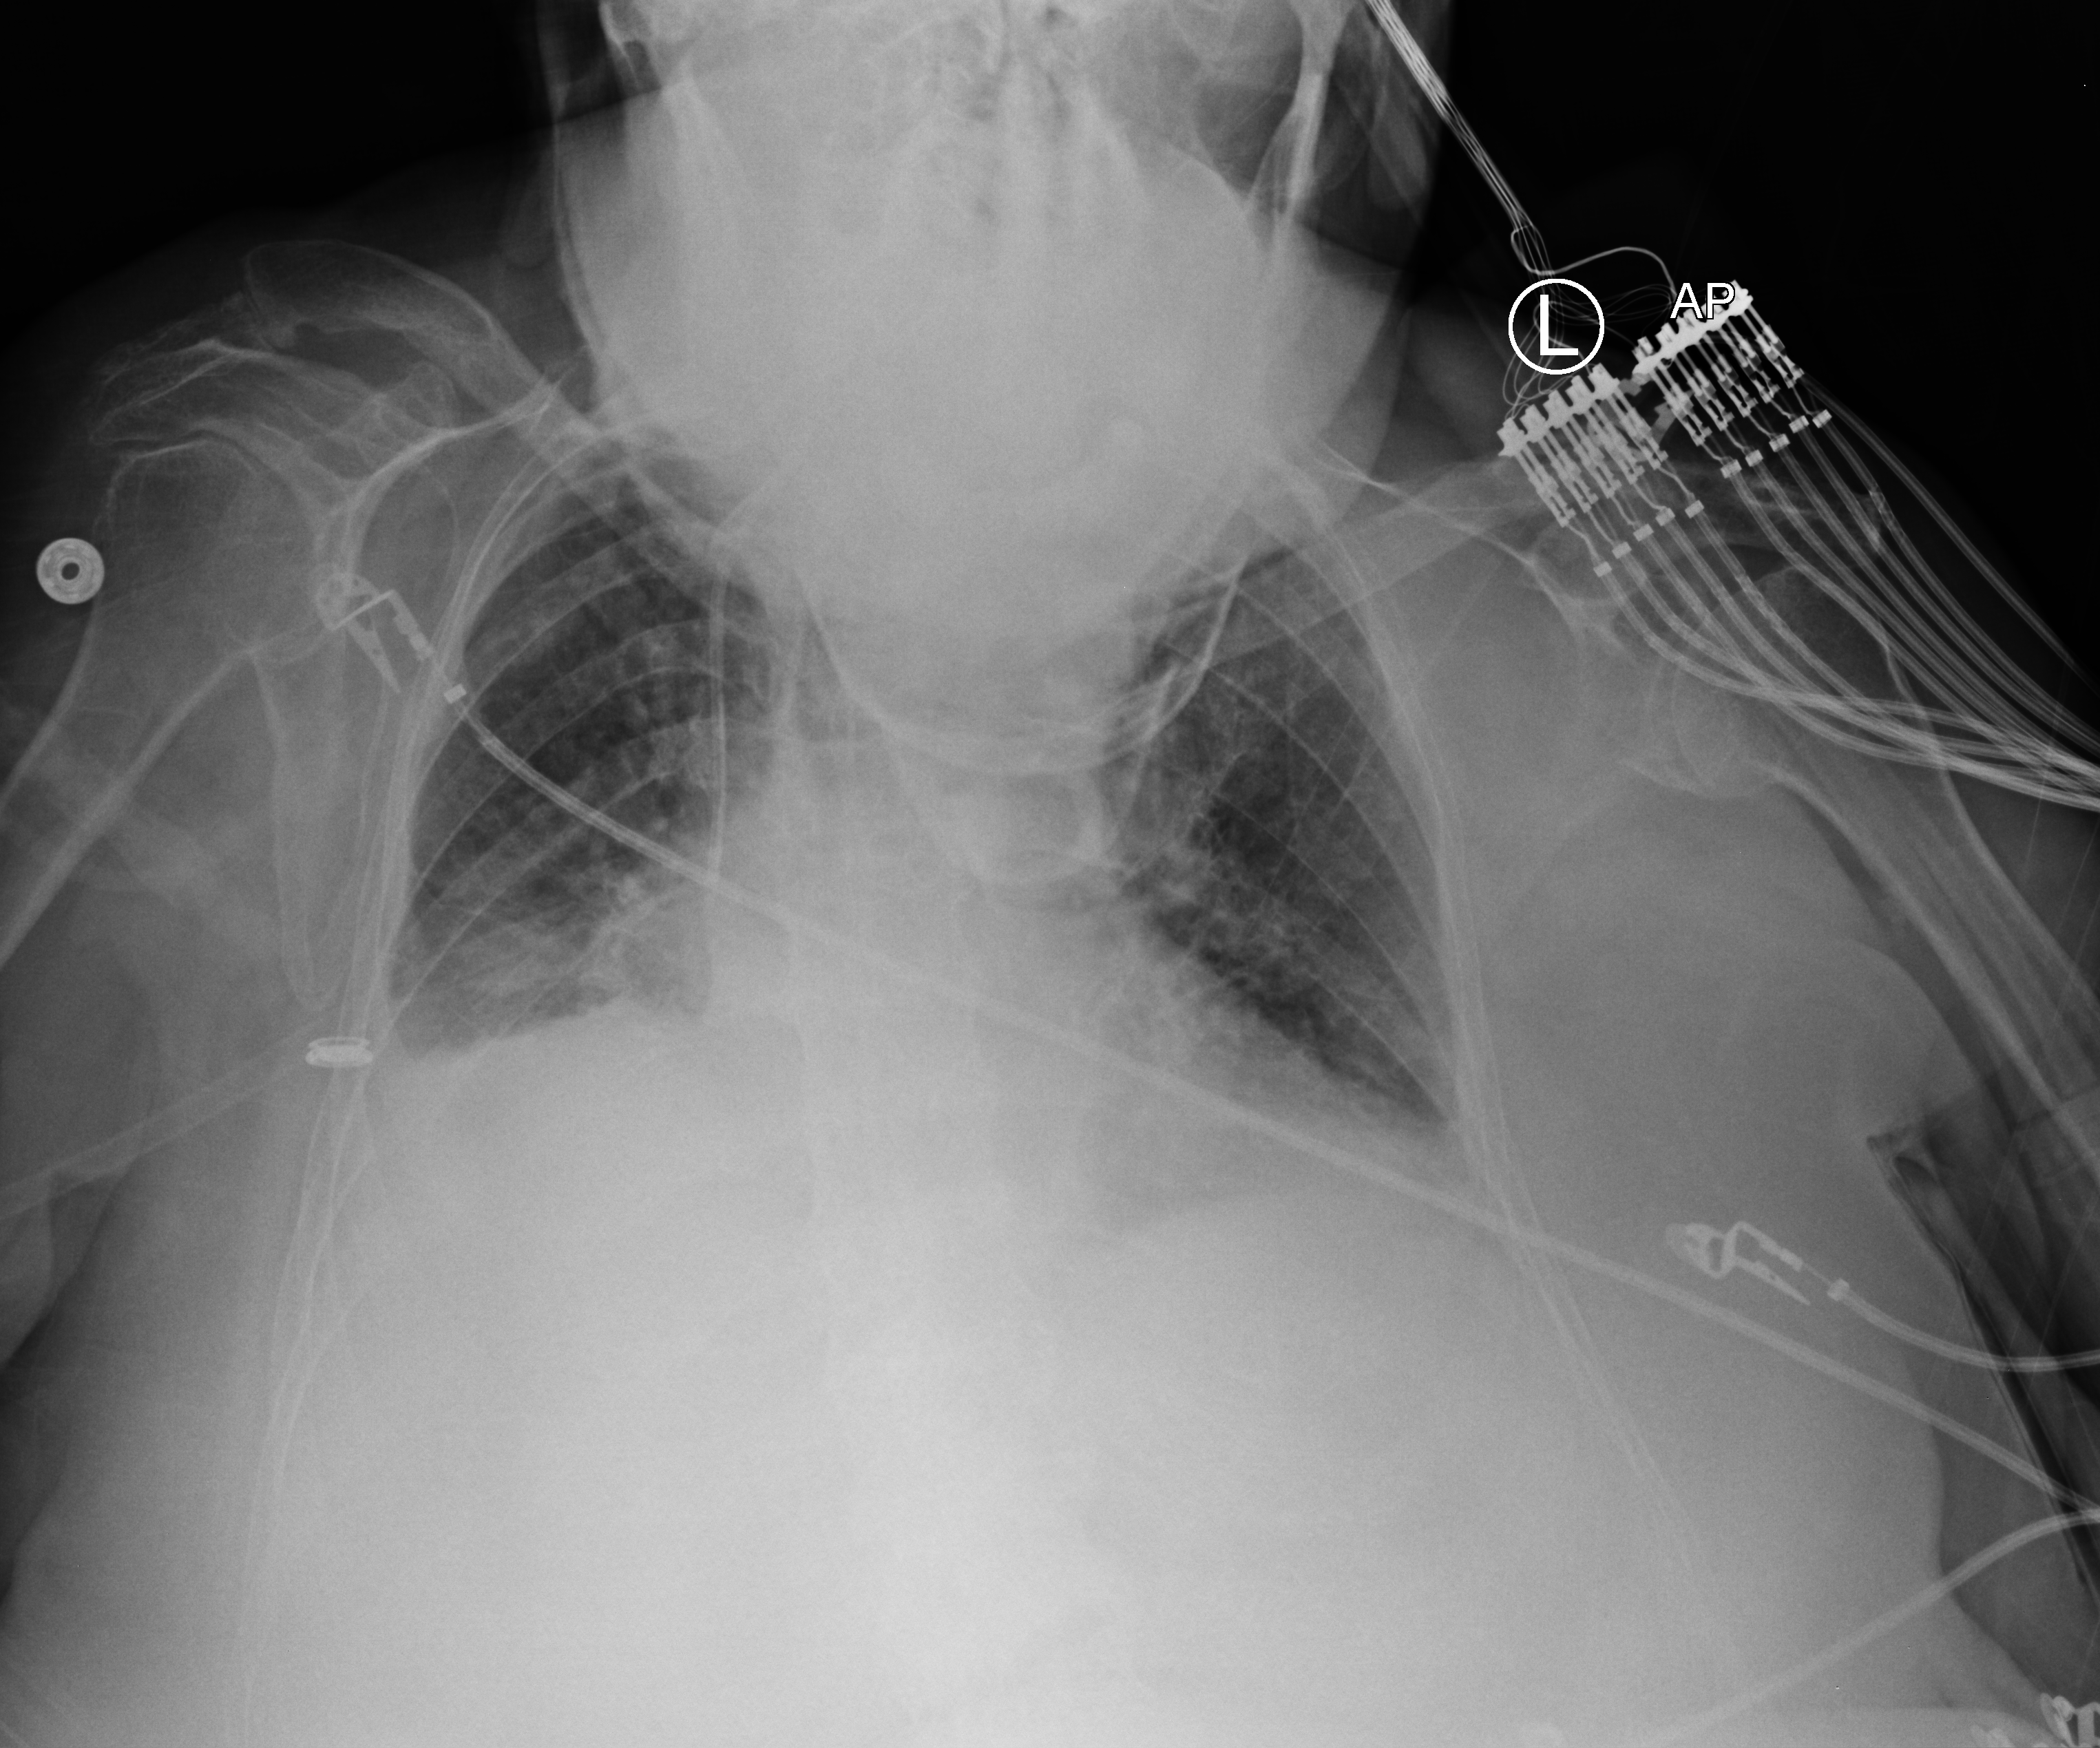
Portable chest radiograph; anteroposterior (AP) projection. Female patient hospitalised with COVID-19, age 75–90 years.
Admission-level facts for this patient (not findings on this image; timing relative to this image not recorded): COPD (admission record): yes.